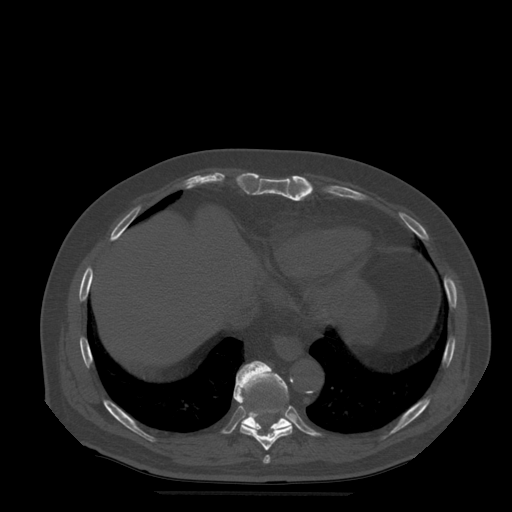
CT including the spine, one axial slice; position 281 of 522 along the scan axis; bone window (W 1800 / L 400 HU); 1.25 mm slice thickness; 512 × 512 image matrix. Patient age 72 years. From the clinical record (not read from this slice): primary cancer: prostate.
Annotated regions visible in this slice (semi-automatically segmented with operator editing):
- T10 vertebra: box from (x=236, y=361) to (x=291, y=431) px
- T8 vertebra: (x=264, y=456)–(x=271, y=464)
- T9 vertebra: (x=234, y=366)–(x=293, y=451)